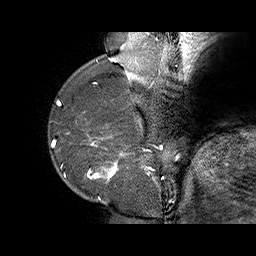
Breast MRI (dynamic contrast-enhanced), one sagittal slice. Slice 14 of 70 in the series (ordered by position). Dynamic contrast-enhanced series, time point 2 of 6 at this slice position (early post-contrast). 1.5 T. TE 4.5 ms, TR 32.4 ms. 256 × 256 image matrix. Female patient. From the clinical record (not read from this slice): setting: breast cancer imaged before/during neoadjuvant chemotherapy; receptor status: HR-positive, HER2-negative.
Outlined on this slice (semi-automatic segmentation, software-assisted and operator-edited):
- analysis volume of interest (the breast-tissue region the enhancement analysis was run in; not a lesion): bounding box [x1, y1, x2, y2] px = [71, 128, 159, 202]
- tumour enhancement mask (voxels above the 100 % enhancement threshold inside the analysis volume of interest): [87, 136, 156, 200]